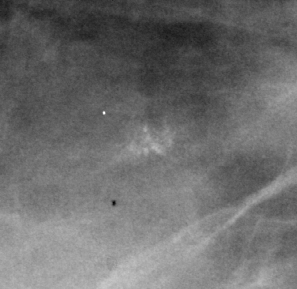
Crop from a digitized film mammogram around one marked abnormality; right breast; CC view.
- Marked abnormality: calcifications, morphology pleomorphic, distribution clustered; BI-RADS assessment category 4; subtlety rating 3 on a 1 (subtle) to 5 (obvious) scale; pathology result (as recorded, not read from the image): benign.